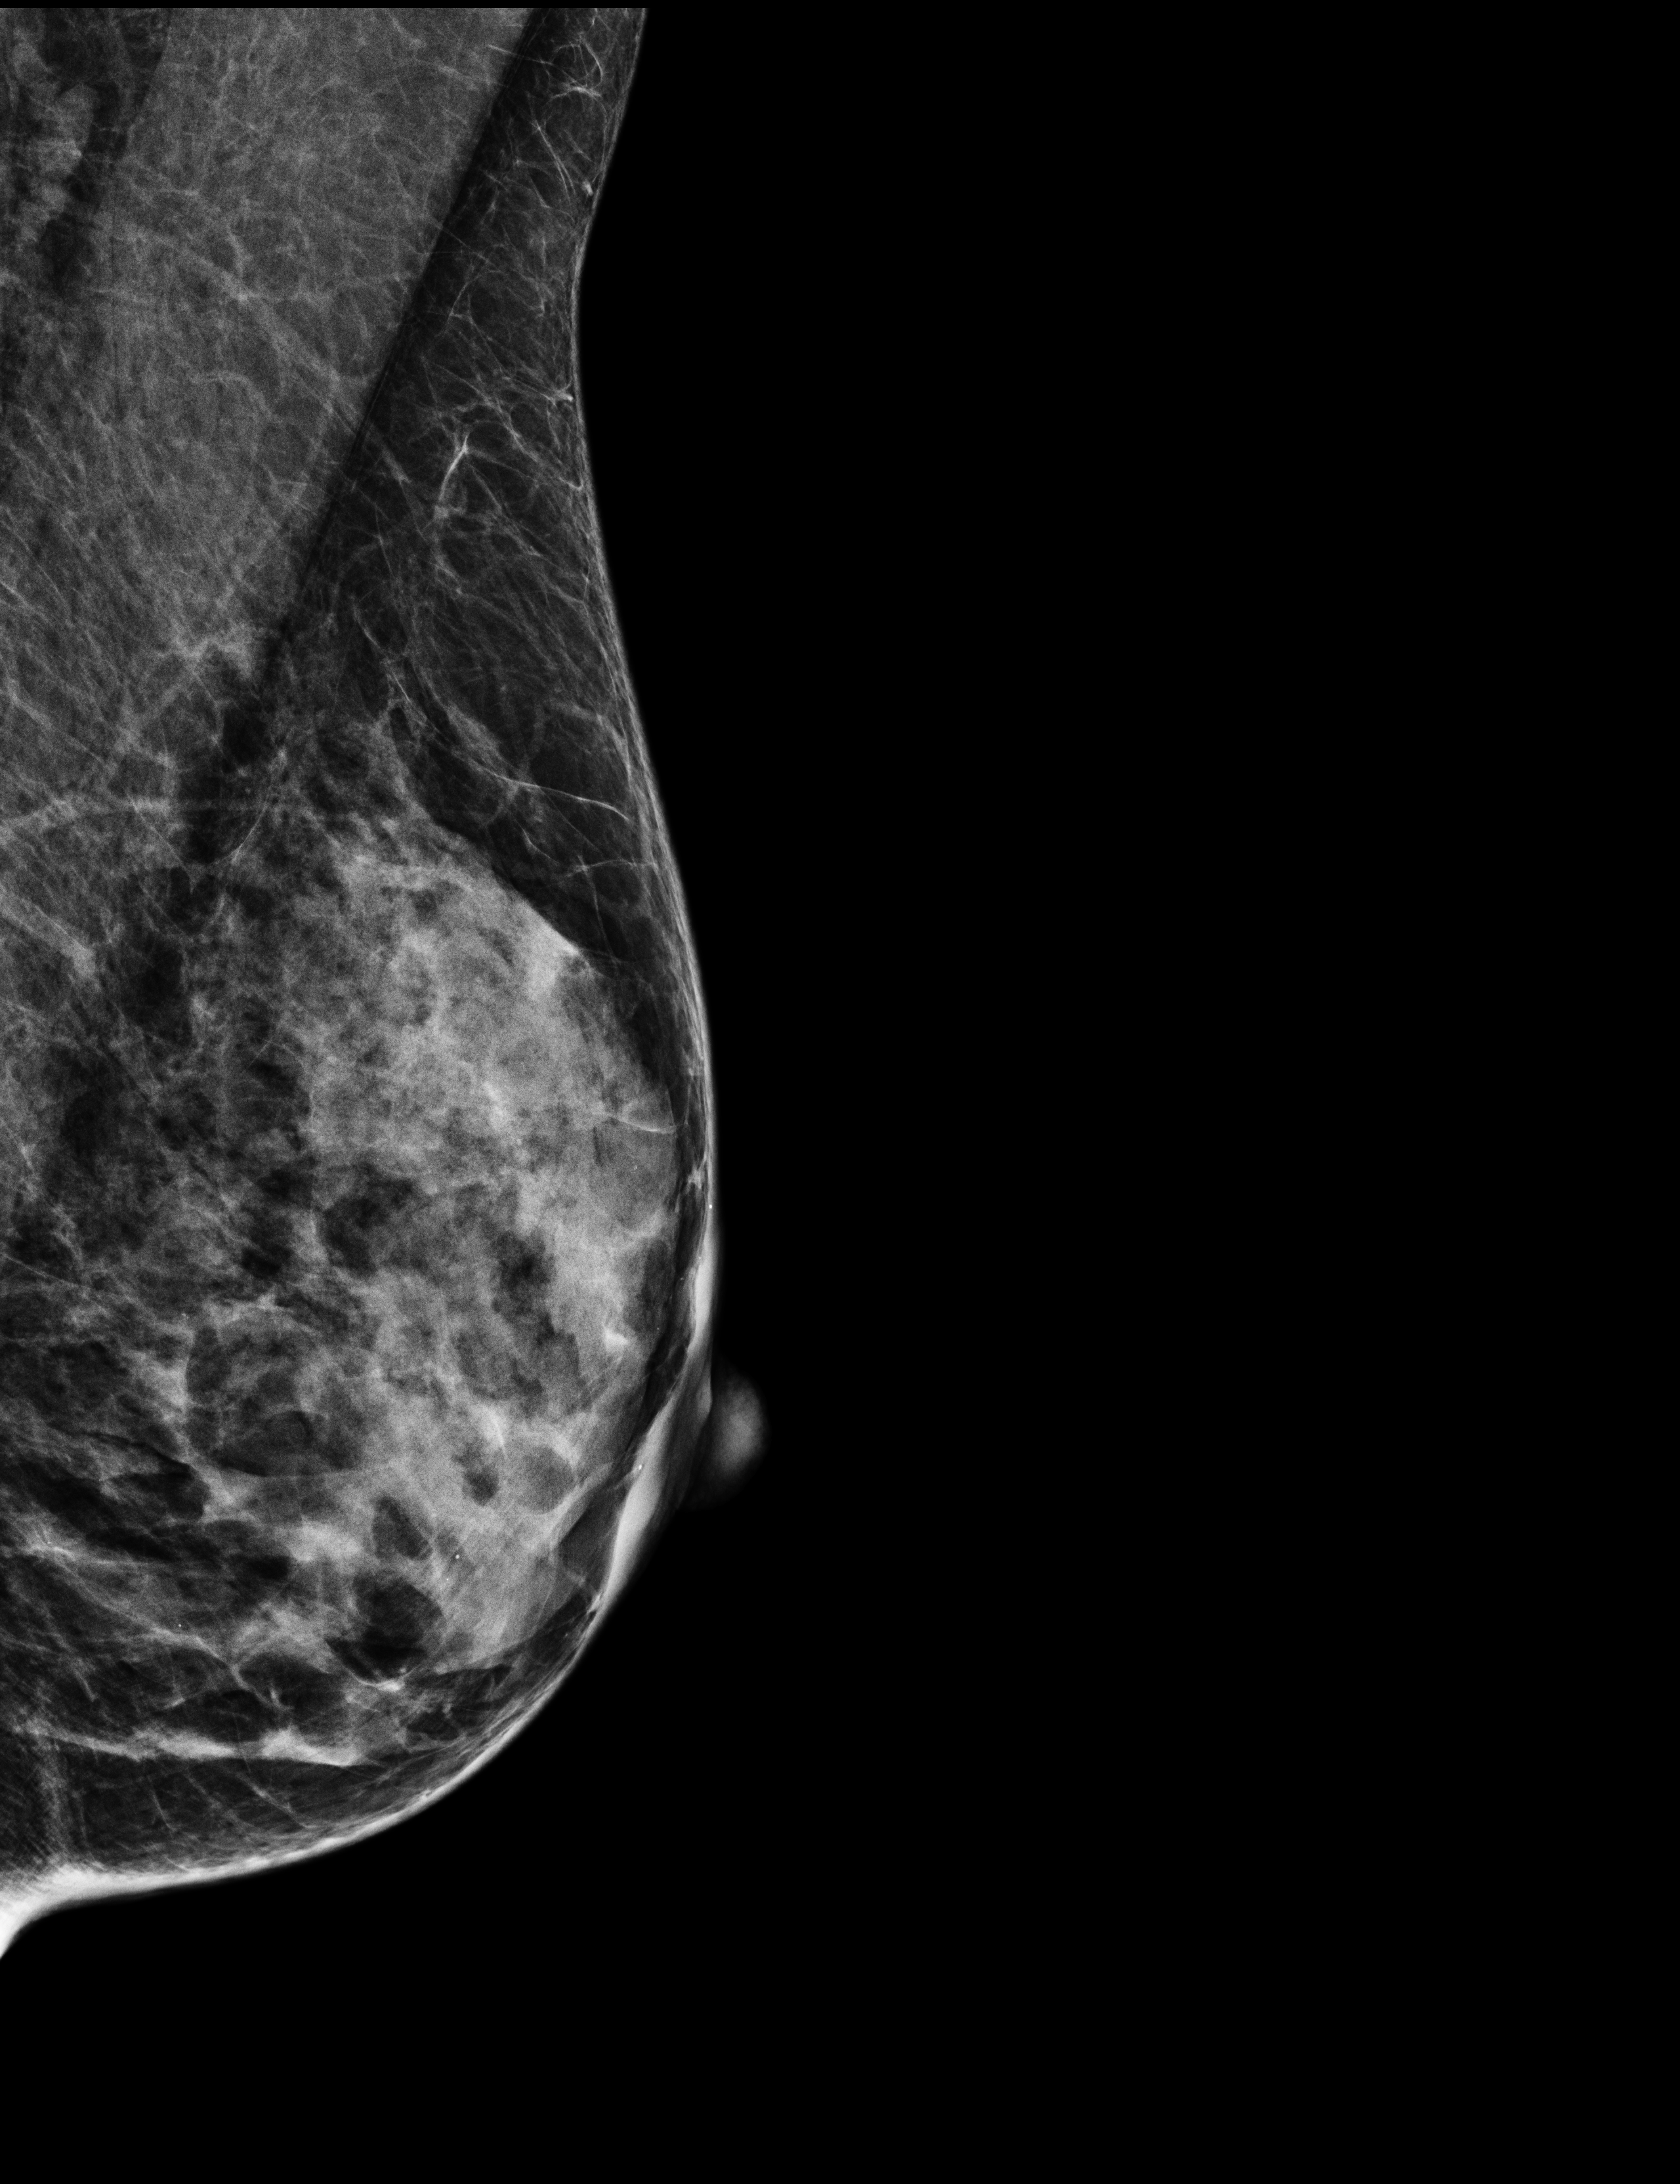
Screening examination; compressed breast thickness 40 mm; system: Selenia Dimensions. Patient: female, 57 years.
Image type: full-field digital mammogram. Breast: left. Projection: mediolateral oblique (MLO) view.